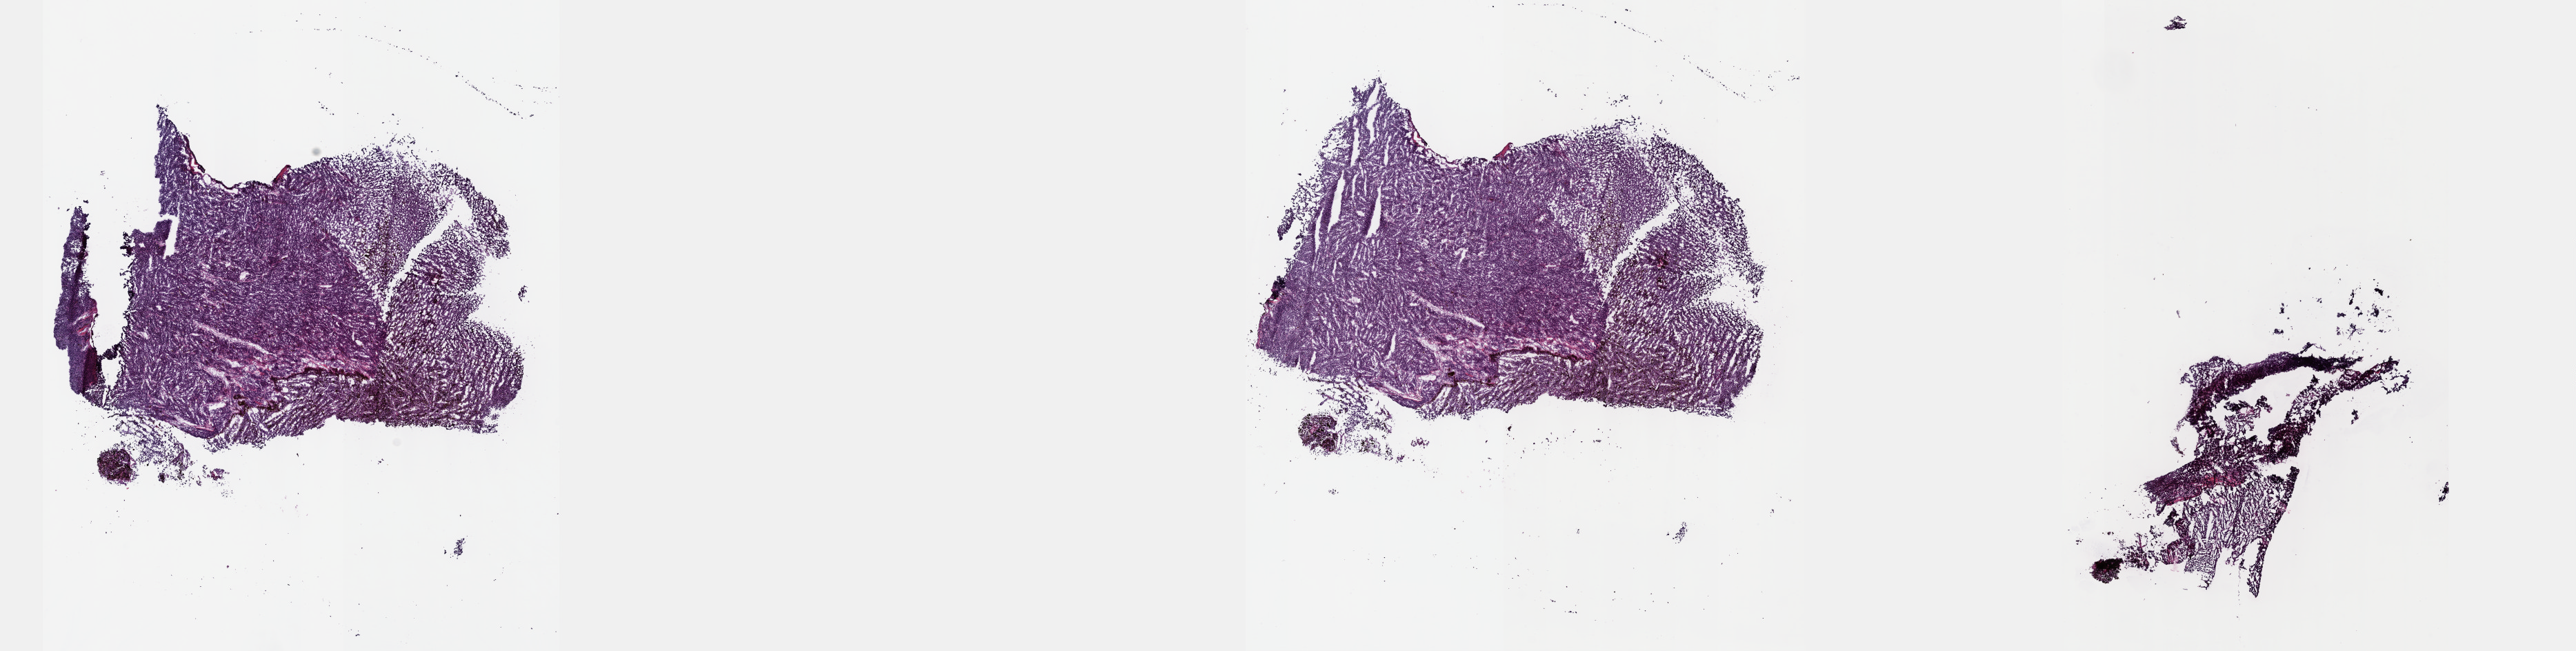
H&E whole-slide image, low-resolution overview of the scanned area, about 30.2 x 7.6 mm (from a 40x scan); frozen section from the top of the tissue portion; sample: primary tumour, uvea. Patient: male, age at initial diagnosis 56 years. Pathologist review of this section (percent, as recorded): tumour cells 90%, tumour nuclei 90%, normal cells 0%, stromal cells 10%, necrosis 0%. Infiltration values recorded for this section: lymphocyte infiltration 0%, monocyte infiltration 0%, neutrophil infiltration 0%.
Pathologic diagnosis: Mixed epithelioid and spindle cell melanoma (choroid). AJCC pathologic stage: IIB (7th edition). Laterality: left.